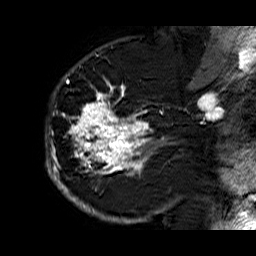
Breast MRI (dynamic contrast-enhanced), one sagittal slice. Position 42 of 60 along the scan axis. Dynamic contrast-enhanced series, time point 2 of 6 at this slice position (early post-contrast). 1.5 T. TE 6.3 ms, TR 32.9 ms. 4 mm slice thickness. 256 × 256 image matrix, field of view 200 × 200 mm. Female patient. Case-level facts recorded for this patient, not image findings: setting: breast cancer imaged before/during neoadjuvant chemotherapy; receptor status: HR-positive, HER2-negative.
Annotated regions visible in this slice (semi-automatically segmented with operator editing):
- analysis volume of interest (the breast-tissue region the enhancement analysis was run in; not a lesion): box from (x=45, y=74) to (x=176, y=210) px
- tumour enhancement mask (voxels above the 100 % enhancement threshold inside the analysis volume of interest): (x=45, y=74)–(x=167, y=210)